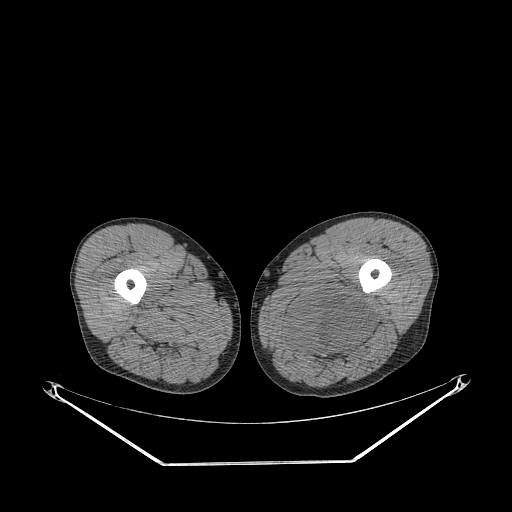
CT of an extremity soft-tissue mass (from a PET/CT study), one axial slice. Reconstruction kernel STANDARD. 140 kVp. Soft-tissue window (W 400 / L 40 HU). 512 × 512 image matrix. Male patient. From the clinical record (not read from this slice): histological type: undifferentiated pleomorphic liposarcoma; grade: high; site of the primary tumour: left thigh.
Structures marked on this image (expert contour drawn on MRI and transferred to this co-registered scan by the dataset authors):
- gross tumour volume including surrounding oedema: bounding box [x1, y1, x2, y2] px = [281, 288, 373, 359]
- gross tumour volume (mass): [290, 292, 371, 350]